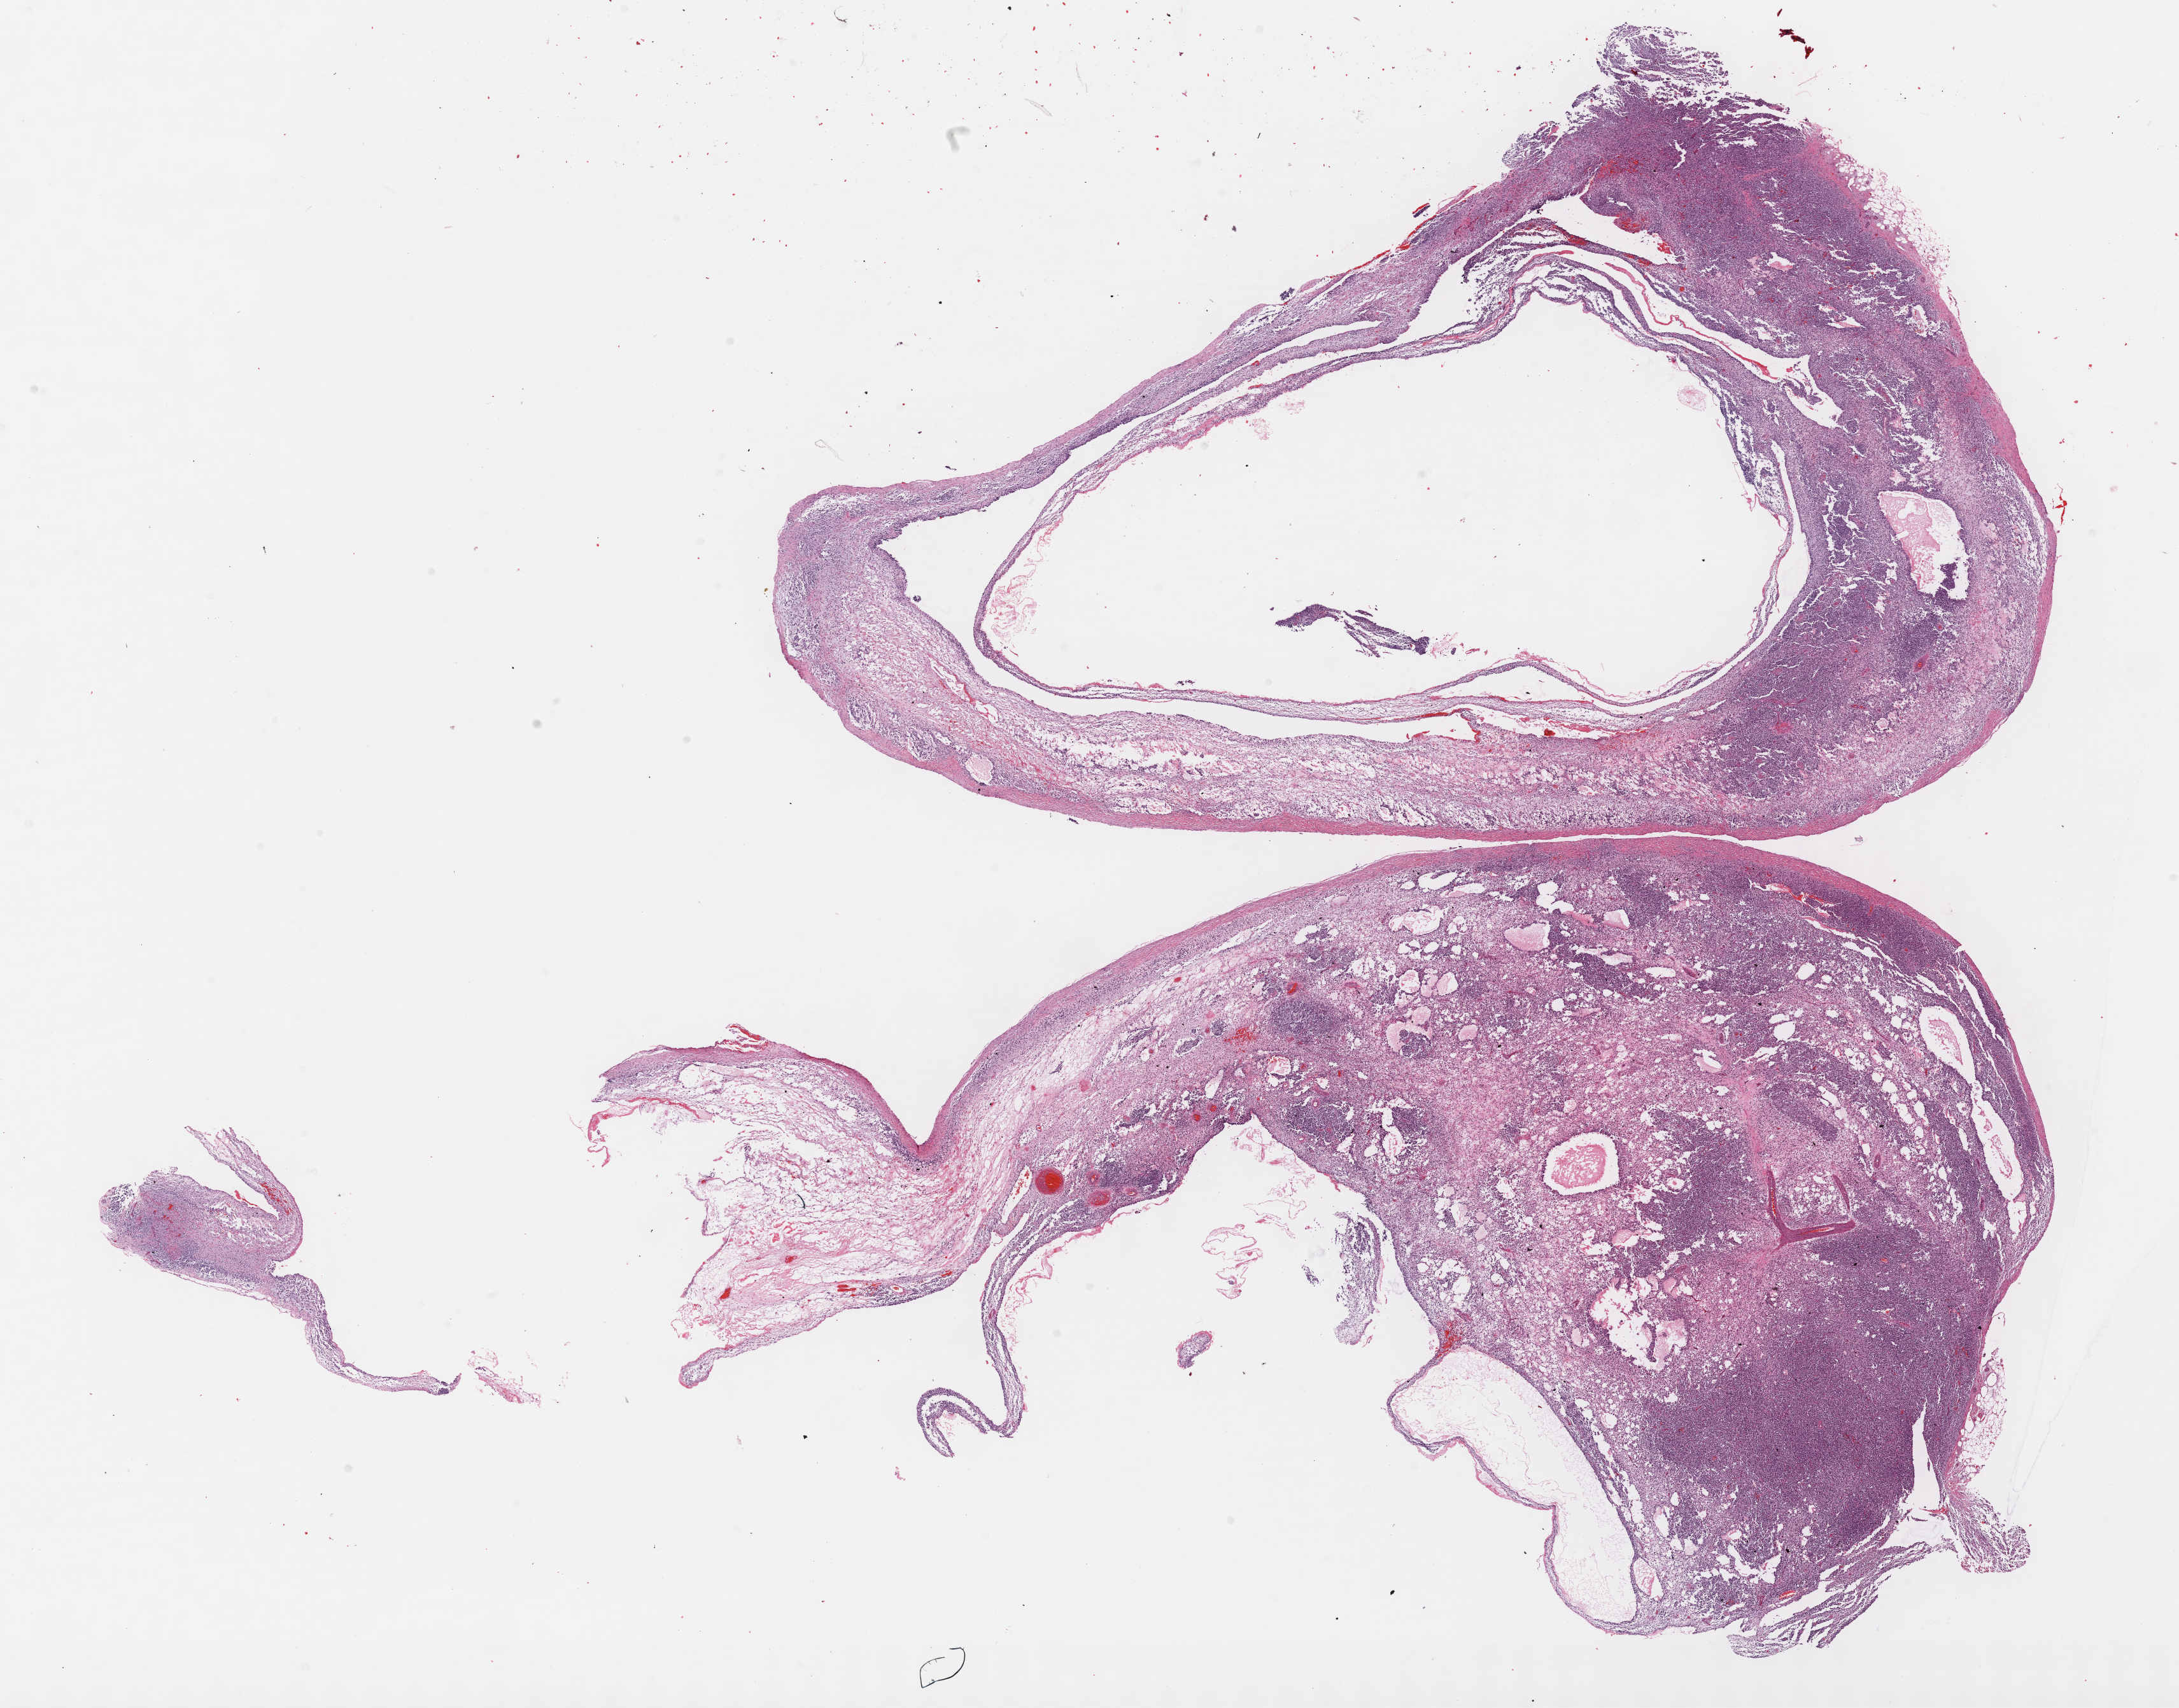
Whole-slide histology image, H&E, low-resolution overview of the scanned area, about 27.7 x 21.7 mm (from a 40x scan), formalin-fixed paraffin-embedded (FFPE) diagnostic section, sample: primary tumour, retroperitoneum and peritoneum. Patient: male, age at initial diagnosis 57 years.
Histologic diagnosis: Dedifferentiated liposarcoma (retroperitoneum).